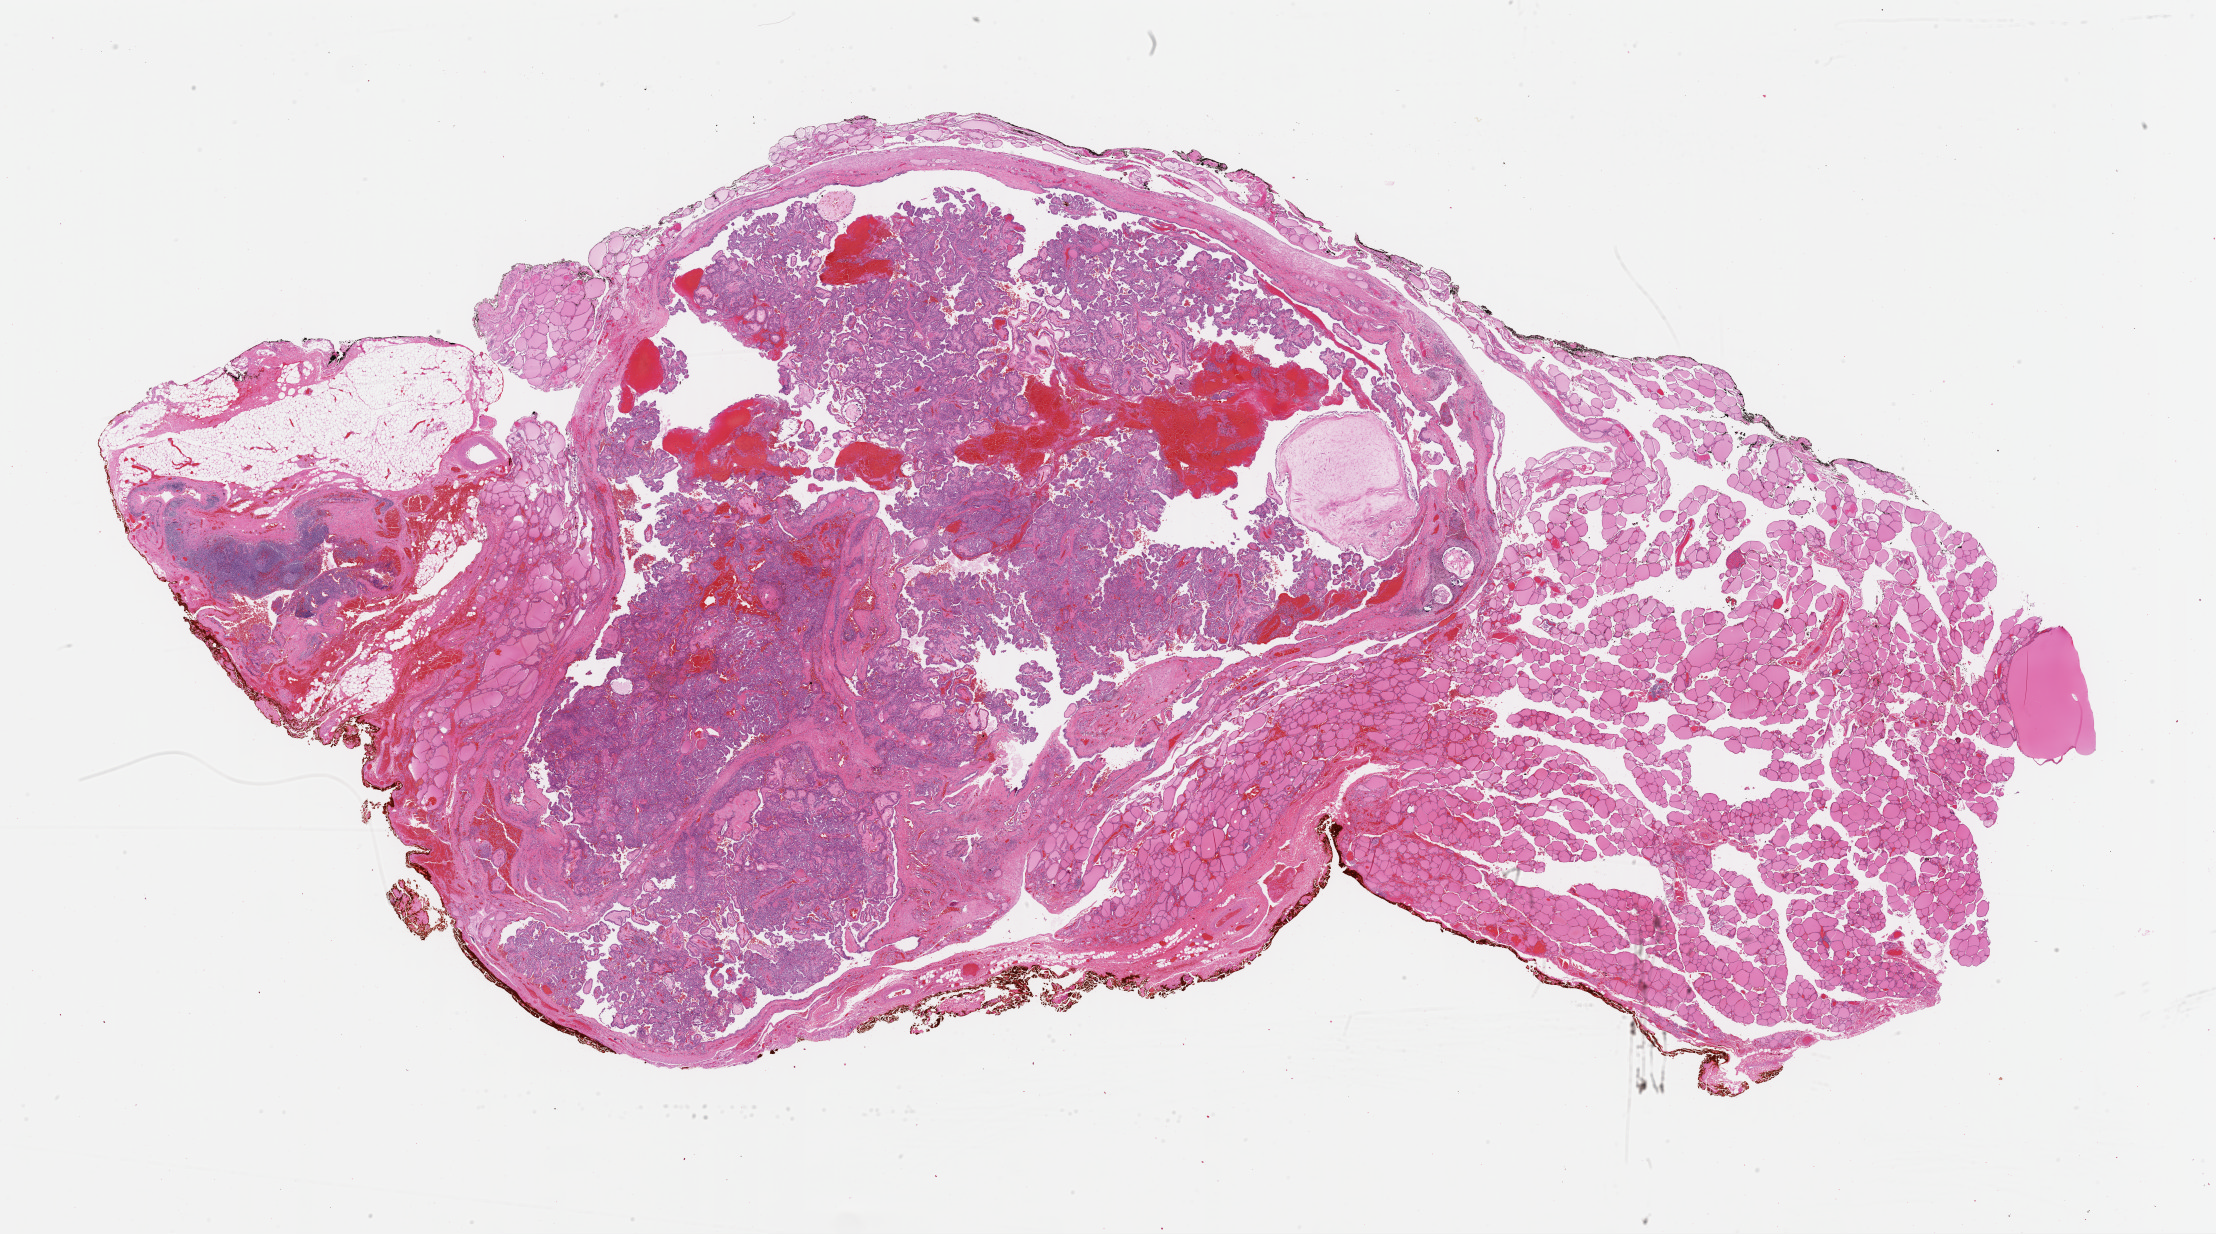
Whole-slide histology image, Hematoxylin and eosin (H&E) stained — shown as a low-resolution overview of the whole scanned area (about 35.0 x 19.5 mm). FFPE section. Primary tumour sample from the thyroid. Female, age 27 years at initial diagnosis.
Diagnosis: Papillary adenocarcinoma, NOS (thyroid gland).